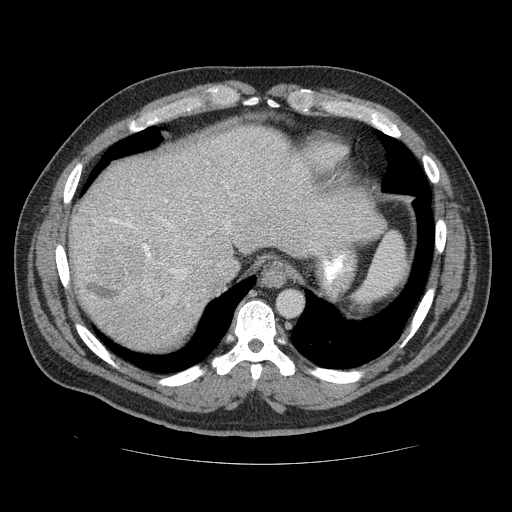
Contrast-enhanced abdominal CT (liver protocol), one axial slice; 120 kVp; soft-tissue window (W 400 / L 40 HU); 2.5 mm slice thickness; 512 × 512 image matrix, field of view 400 × 400 mm. From the clinical record (not read from this slice): diagnosis: hepatocellular carcinoma (patient treated with transarterial chemoembolisation; whether this scan precedes or follows treatment is not stated here); TNM stage (as recorded): Stage-II; Child-Pugh class: B; tumour nodularity: multinodular; tumour size: 4.8 cm.
Structures marked on this image (semi-automatically segmented with operator editing):
- abdominal aorta: box from (x=279, y=292) to (x=301, y=315) px
- liver parenchyma outside the tumour (the mass and vessels are separate outlines, so this box may not span the whole liver): (x=68, y=128)–(x=354, y=346)
- mass: (x=70, y=209)–(x=177, y=302)
- liver vessels: (x=103, y=205)–(x=191, y=259)